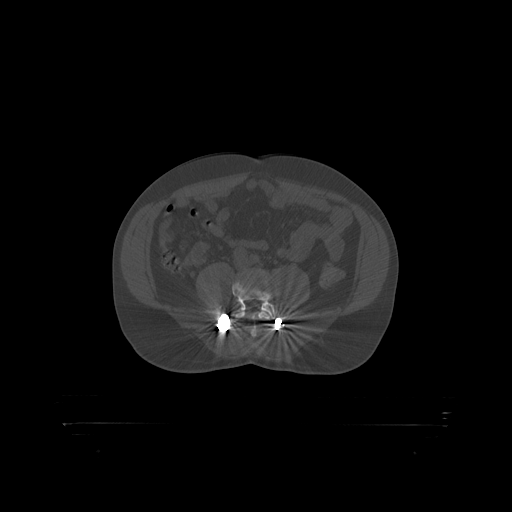
CT including the spine, one axial slice; position 218 of 399 along the scan axis; reconstruction kernel STANDARD; bone window (W 1800 / L 400 HU); 512 × 512 image matrix, field of view 650 × 650 mm. Male patient, age 46 years. From the clinical record (not read from this slice): primary cancer: skin.
Outlined on this slice (semi-automatically segmented with operator editing):
- L4 vertebra: bounding box <235,311,271,319> (left, top, right, bottom; pixels)
- L5 vertebra: <233,280,278,319>